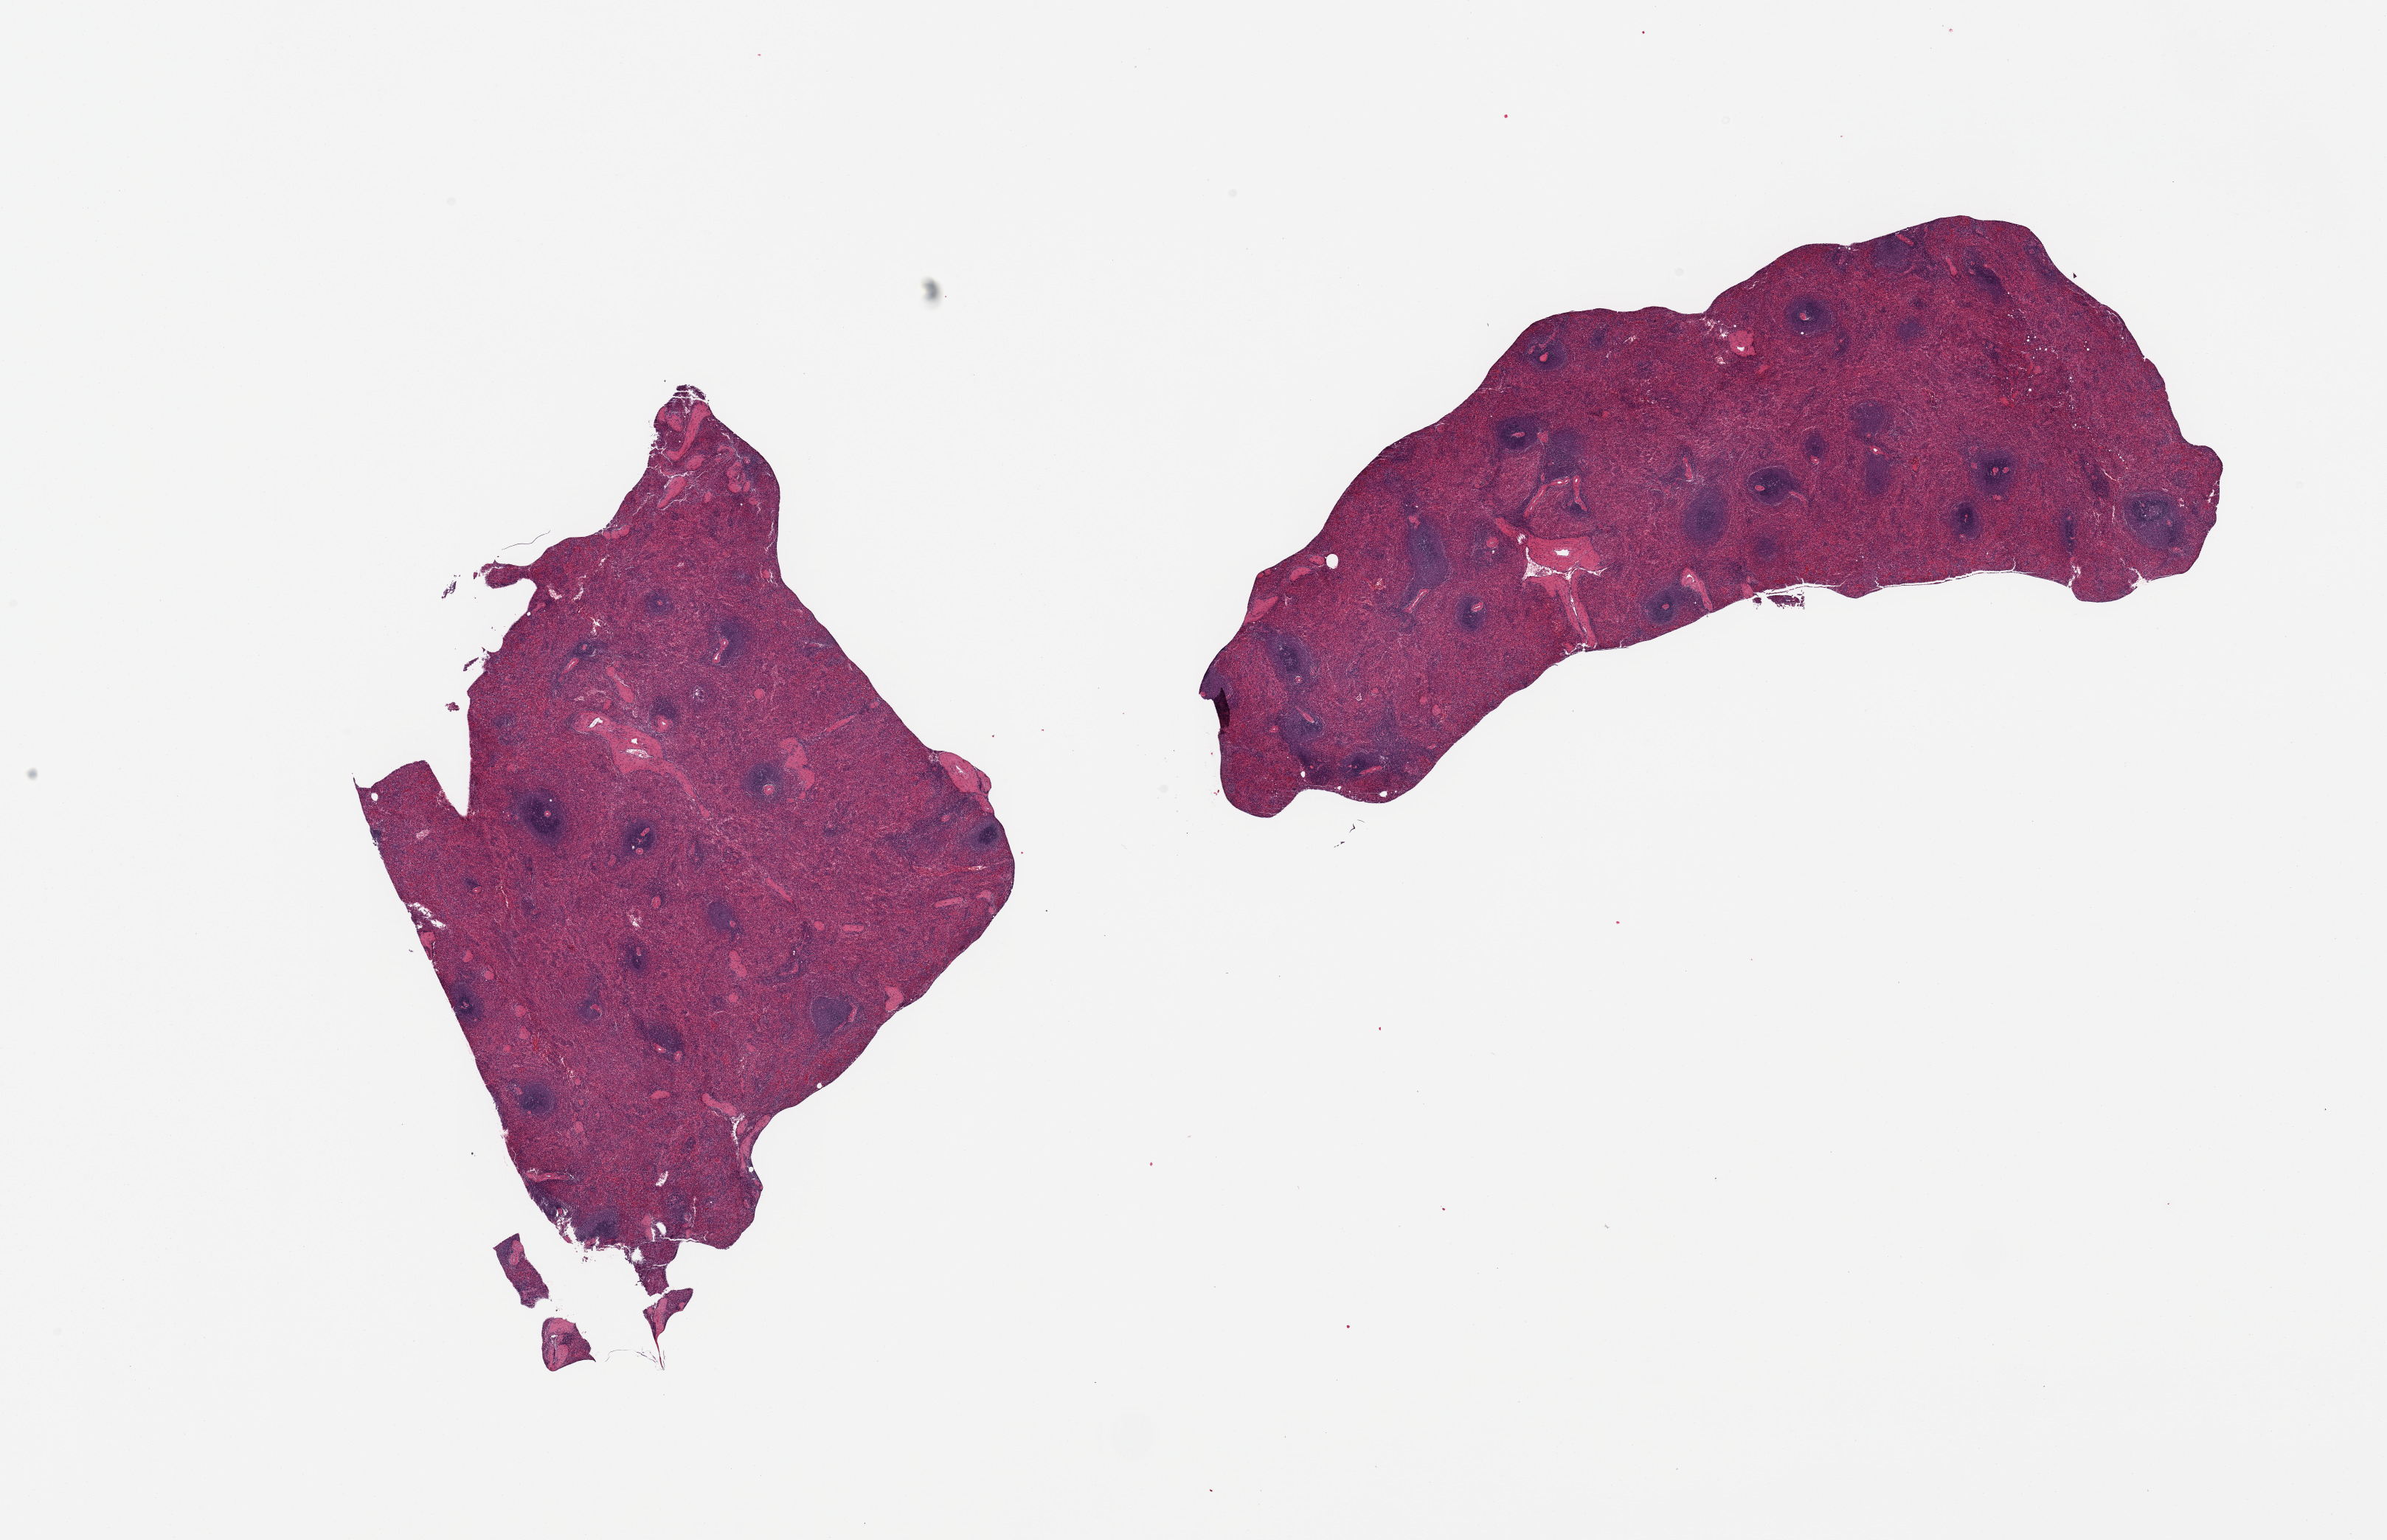
Whole-slide image, haematoxylin and eosin stain, brightfield, a low-resolution overview of the entire scanned area, about 25.6 x 16.5 mm (from a 20x scan). PAXgene-fixed paraffin-embedded (PFPE) section. Sampled site (target tissue): spleen. Tissue donor sample. Female donor.
Pathologist's review note for this sample: 2 pieces, no abnormalities.